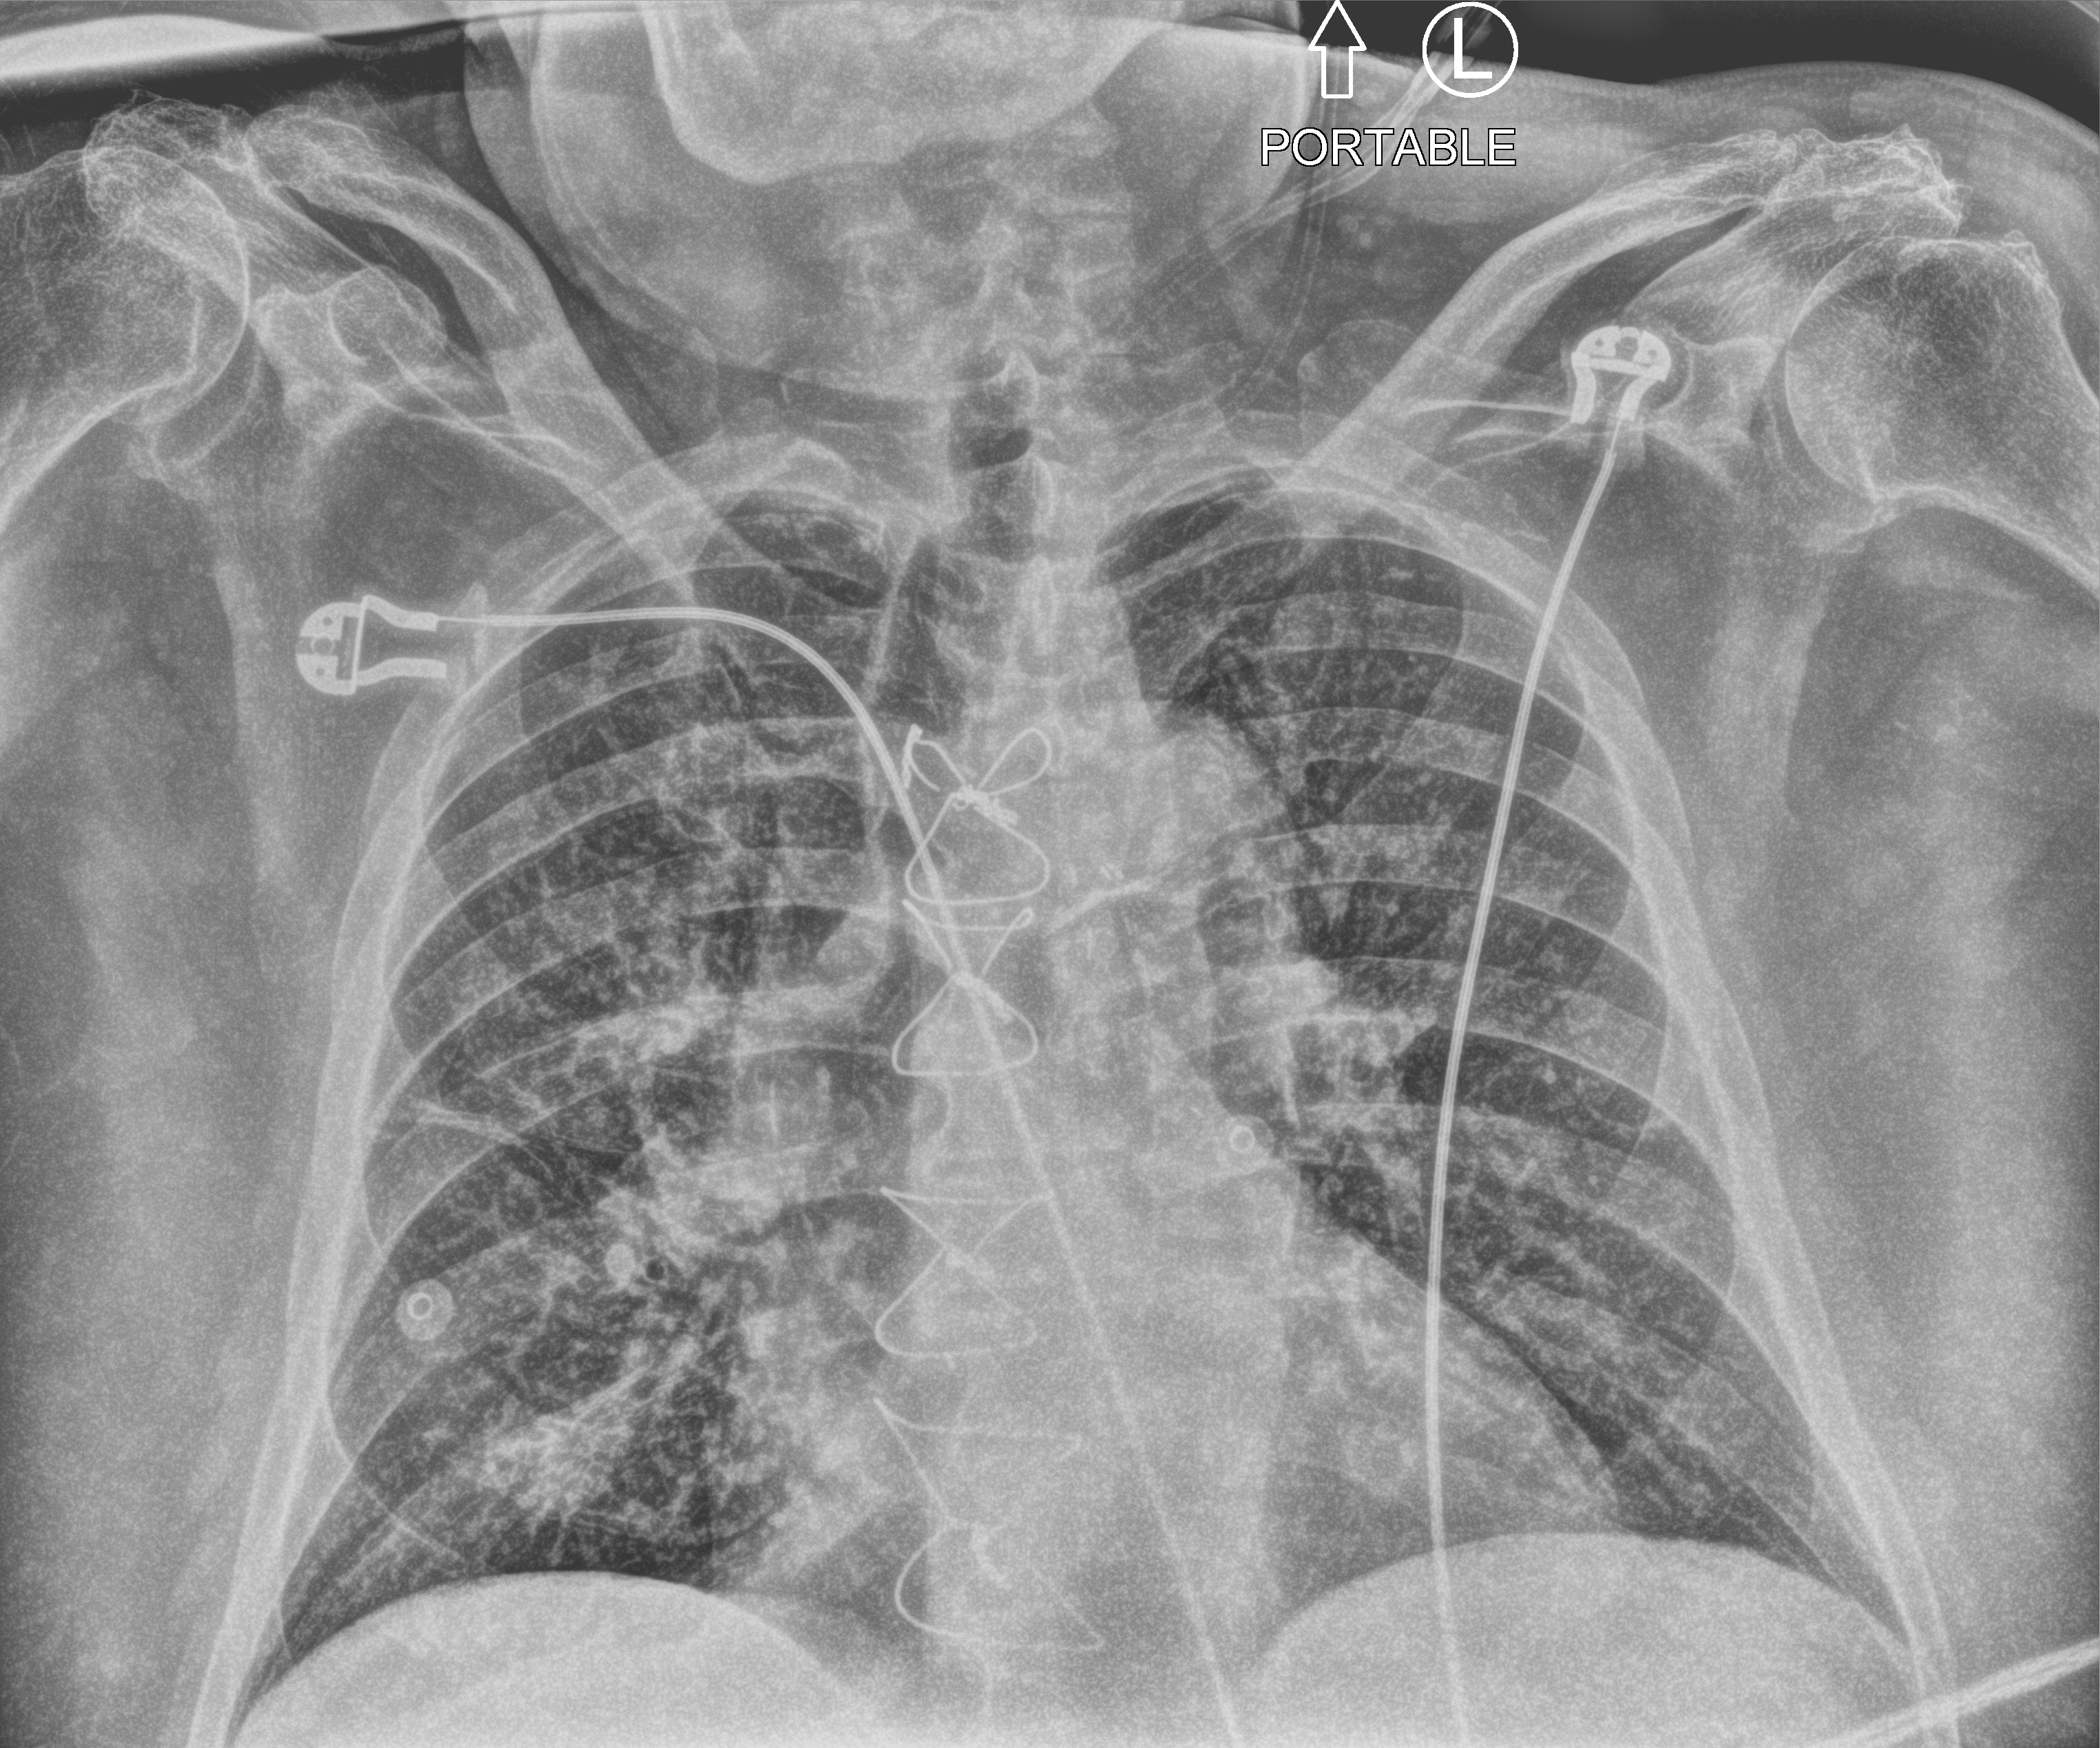
Bedside chest radiograph (computed radiography), anteroposterior (AP) projection. Patient hospitalised with COVID-19; male, aged 75–90 years.
Hospital-stay facts (about this admission, not read from this image; timing relative to this image not recorded):
- hypertension (admission record): yes
- mechanically ventilated during this hospital stay: no